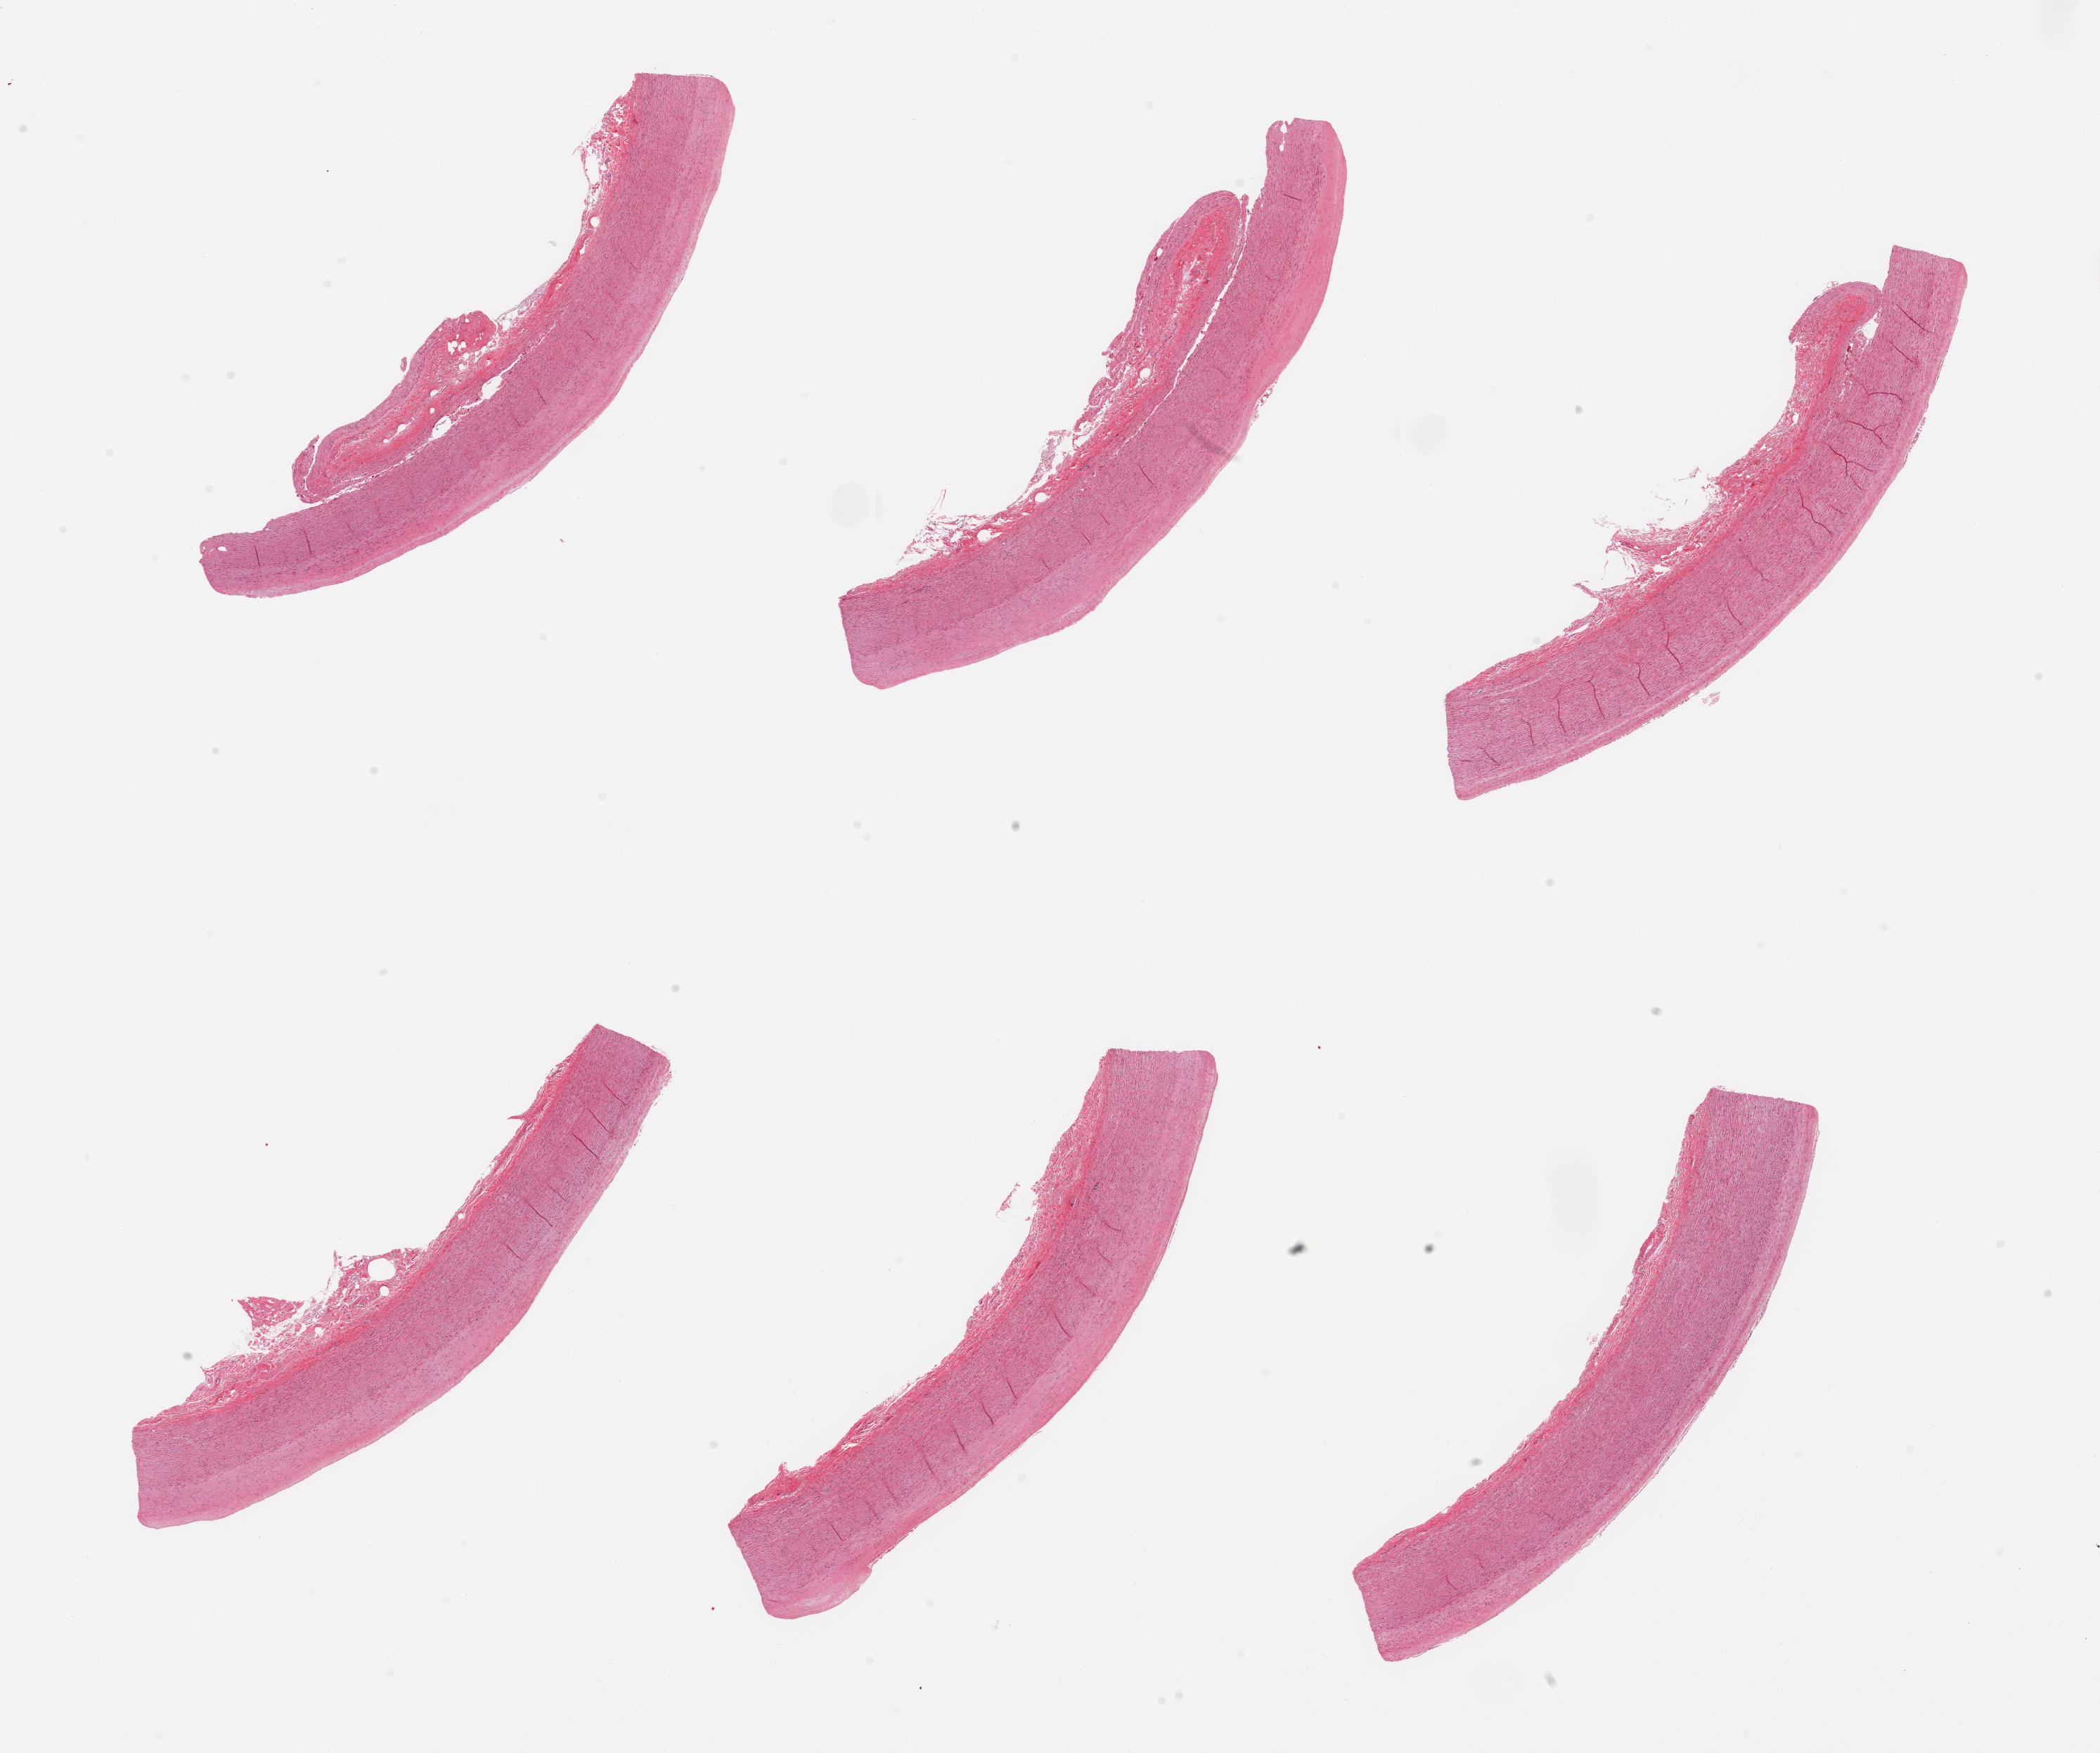
Whole-slide image, H&E stain — a low-resolution overview of the entire scanned area, about 23.6 x 19.7 mm (acquisition: 20x scan); PAXgene-fixed paraffin-embedded (PFPE) section; target tissue: aorta; tissue donor sample. Donor sex: female.
Review note (as recorded): 6 pieces, atherosclerosis.